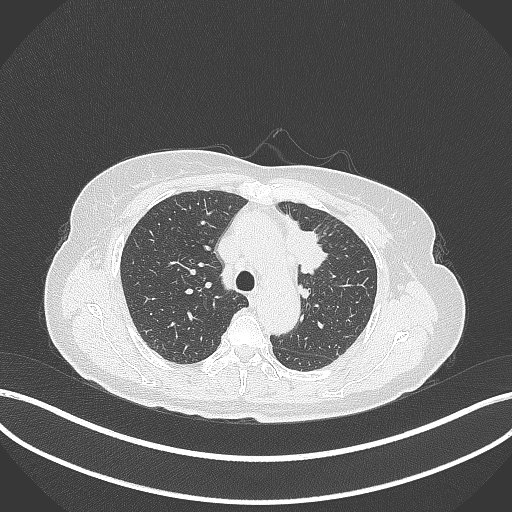
Chest CT, one axial slice; slice 239 of 369 in the series (ordered by position); 120 kVp; lung window (W 1500 / L -600 HU); 1 mm slice thickness; 512 × 512 image matrix. Female patient, age 65 years. From the clinical record (not read from this slice): clinical TNM (as recorded): T2a N0 M0.
Outlined on this slice (rectangle marked by the reading radiologist):
- lung tumour (recorded histology: adenocarcinoma): bounding box <281,211,330,276> (left, top, right, bottom; pixels)